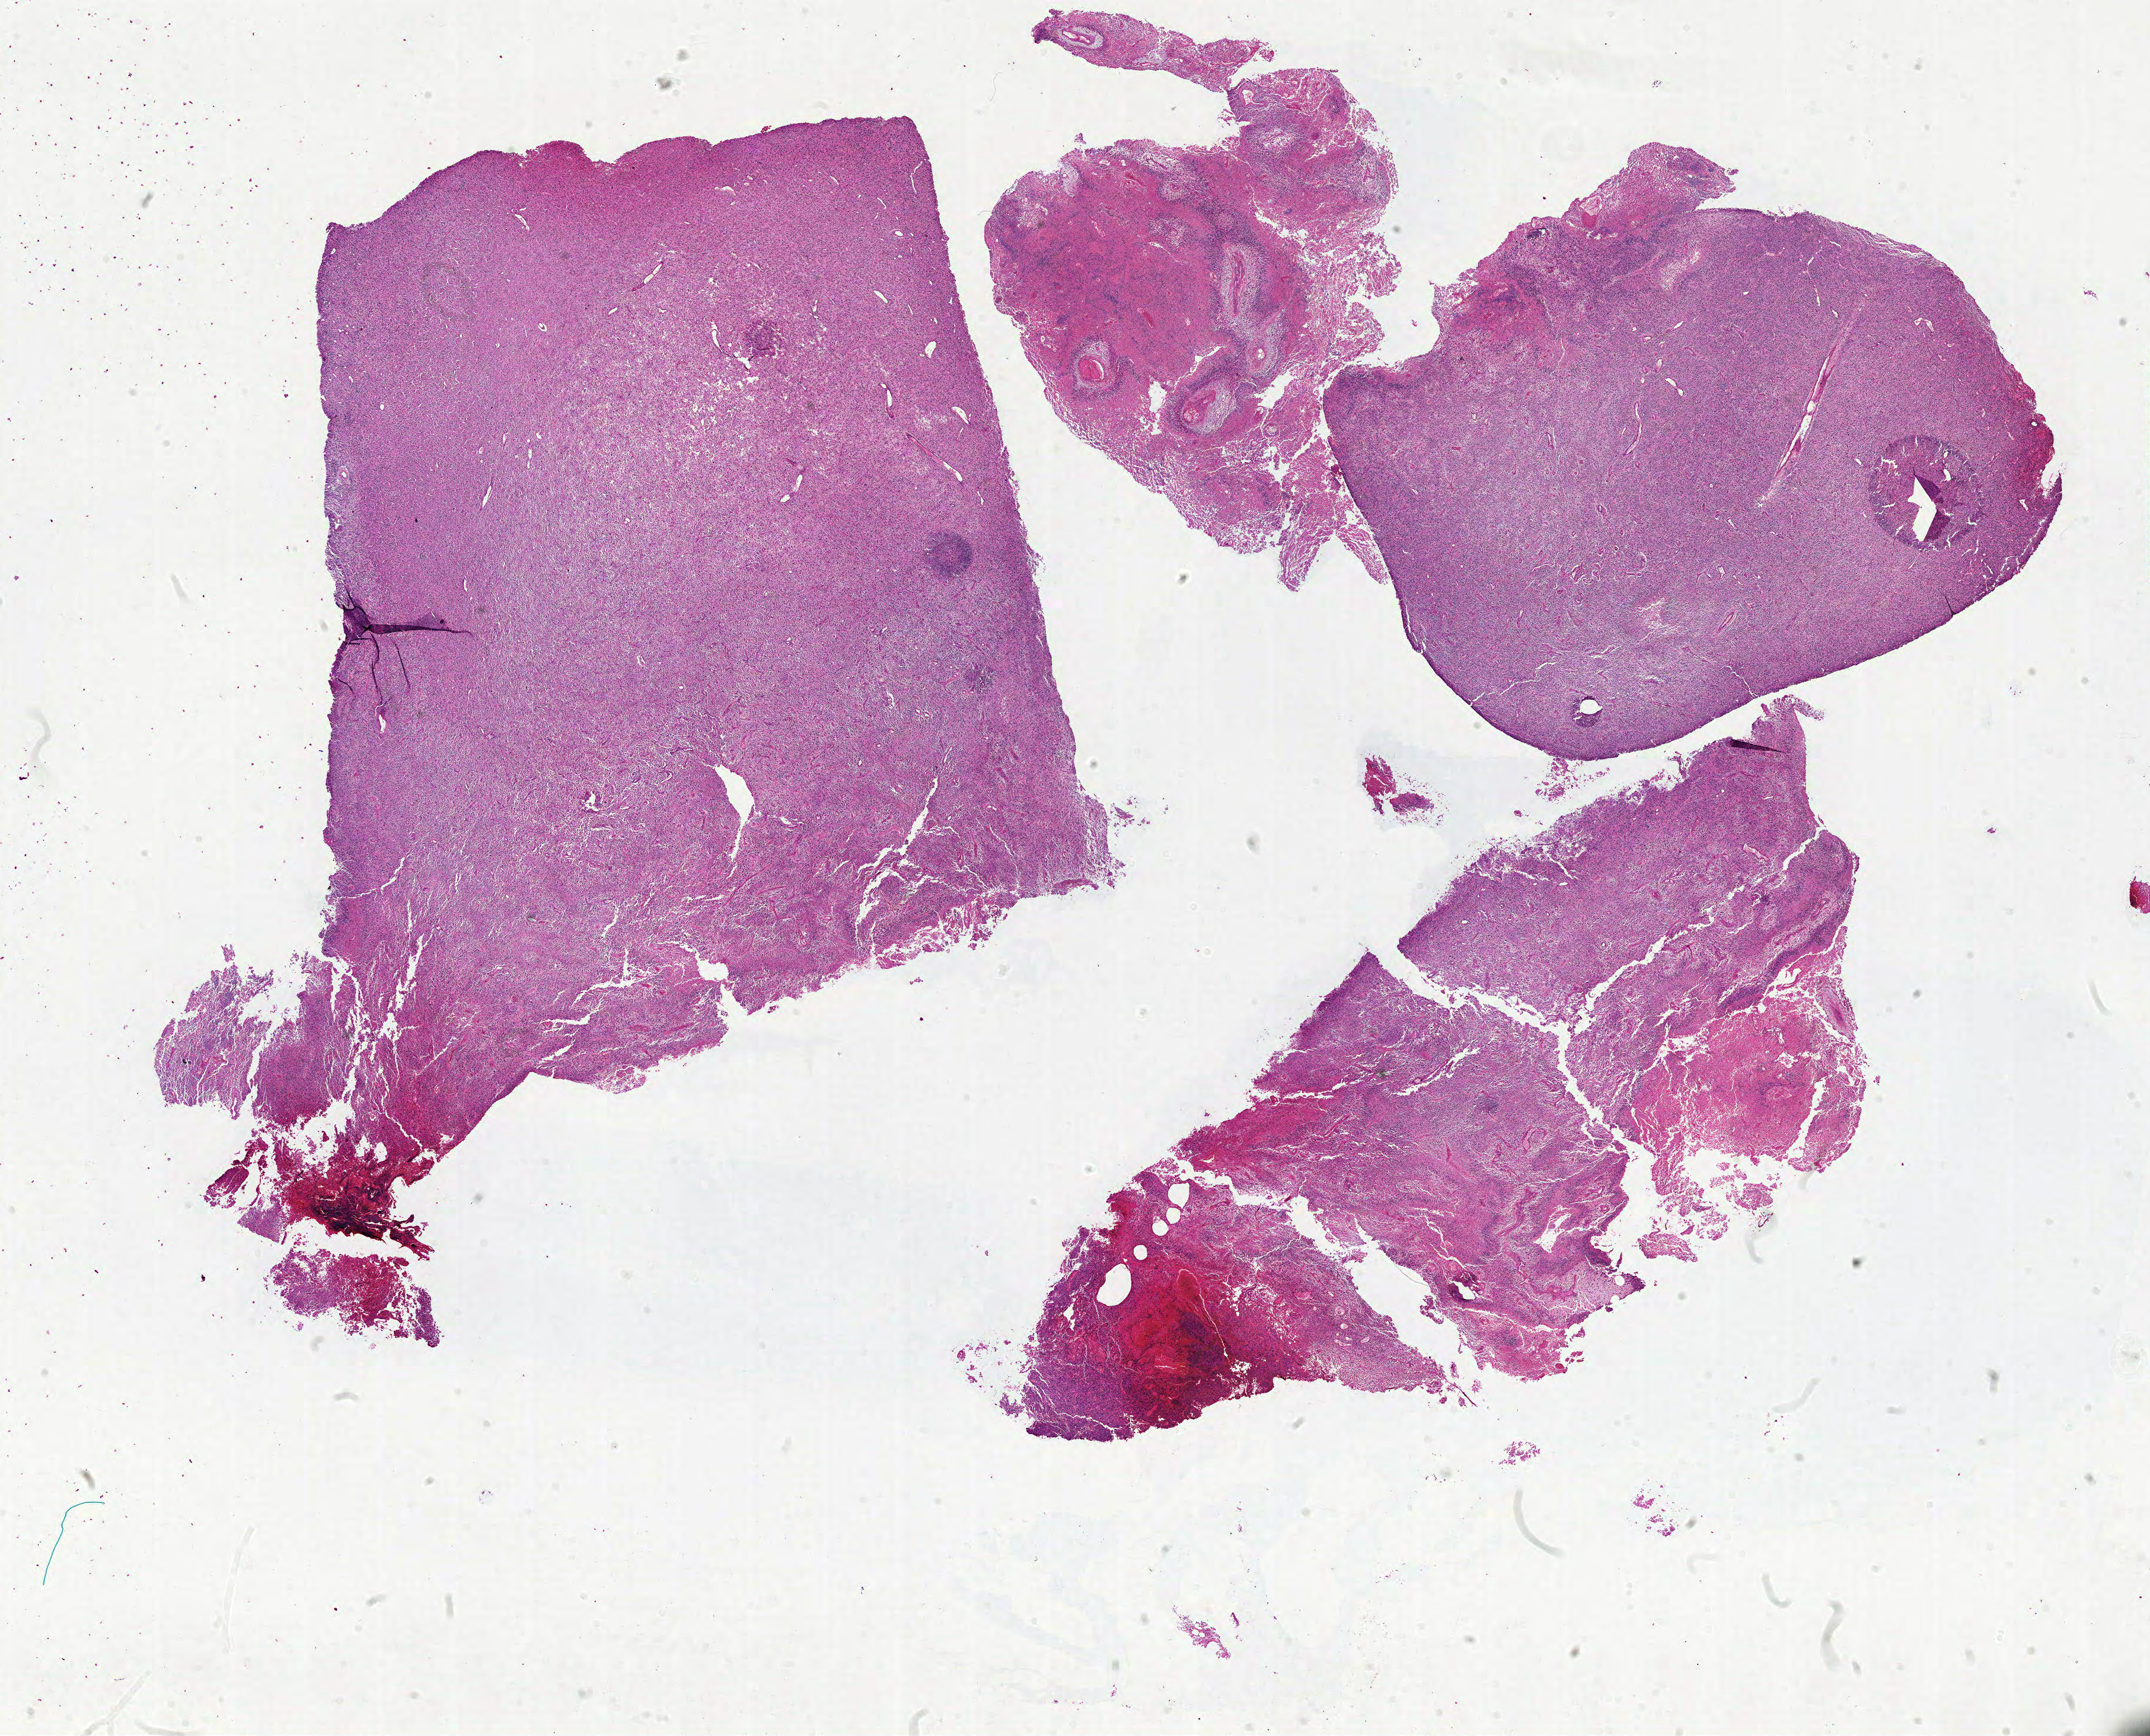
H&E-stained whole-slide image — a low-resolution overview of the entire scanned area, about 29.0 x 23.4 mm (acquisition: 20x scan). Formalin-fixed paraffin-embedded (FFPE) diagnostic section. Brain, primary tumour sample. Patient: female, age at initial diagnosis 47 years.
Diagnosis: Glioblastoma.